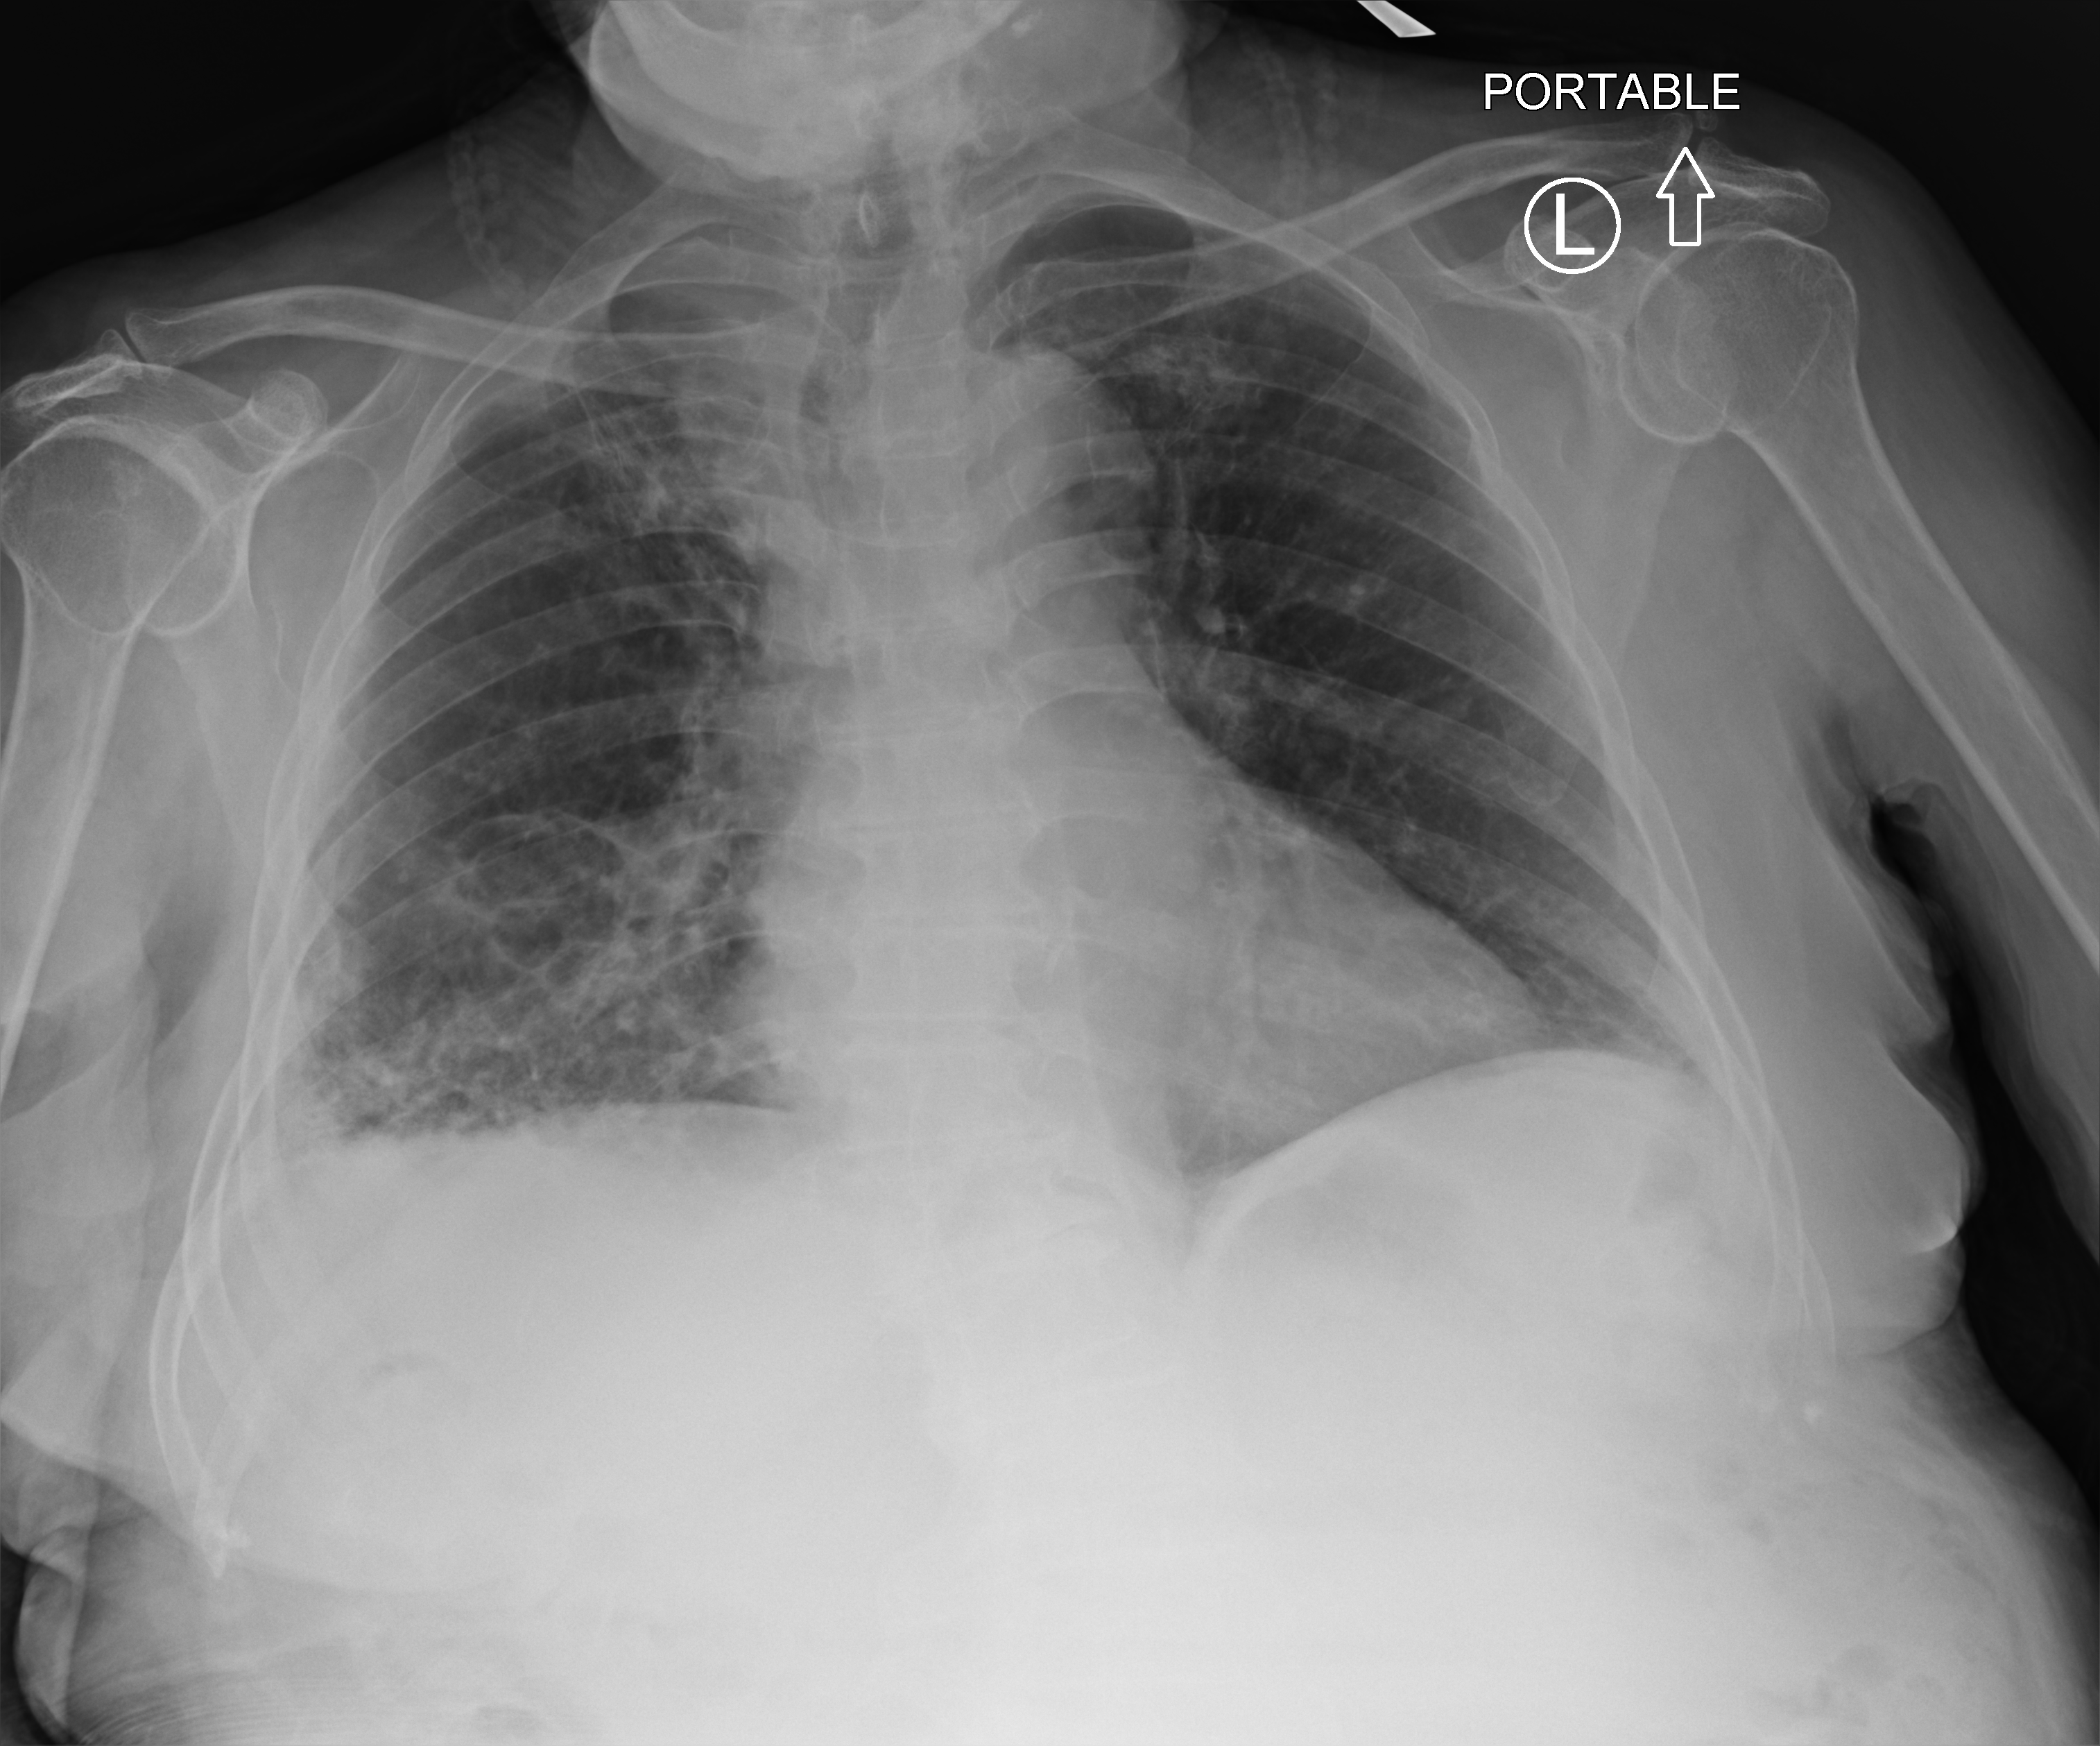
Bedside chest radiograph (computed radiography), anteroposterior (AP) projection. Patient hospitalised with COVID-19; female, aged 75–90 years.
Admission-level facts for this patient (not findings on this image; timing relative to this image not recorded): length of hospital stay: 1 day; mechanically ventilated during this hospital stay: no; admitted to intensive care during this hospital stay: no.